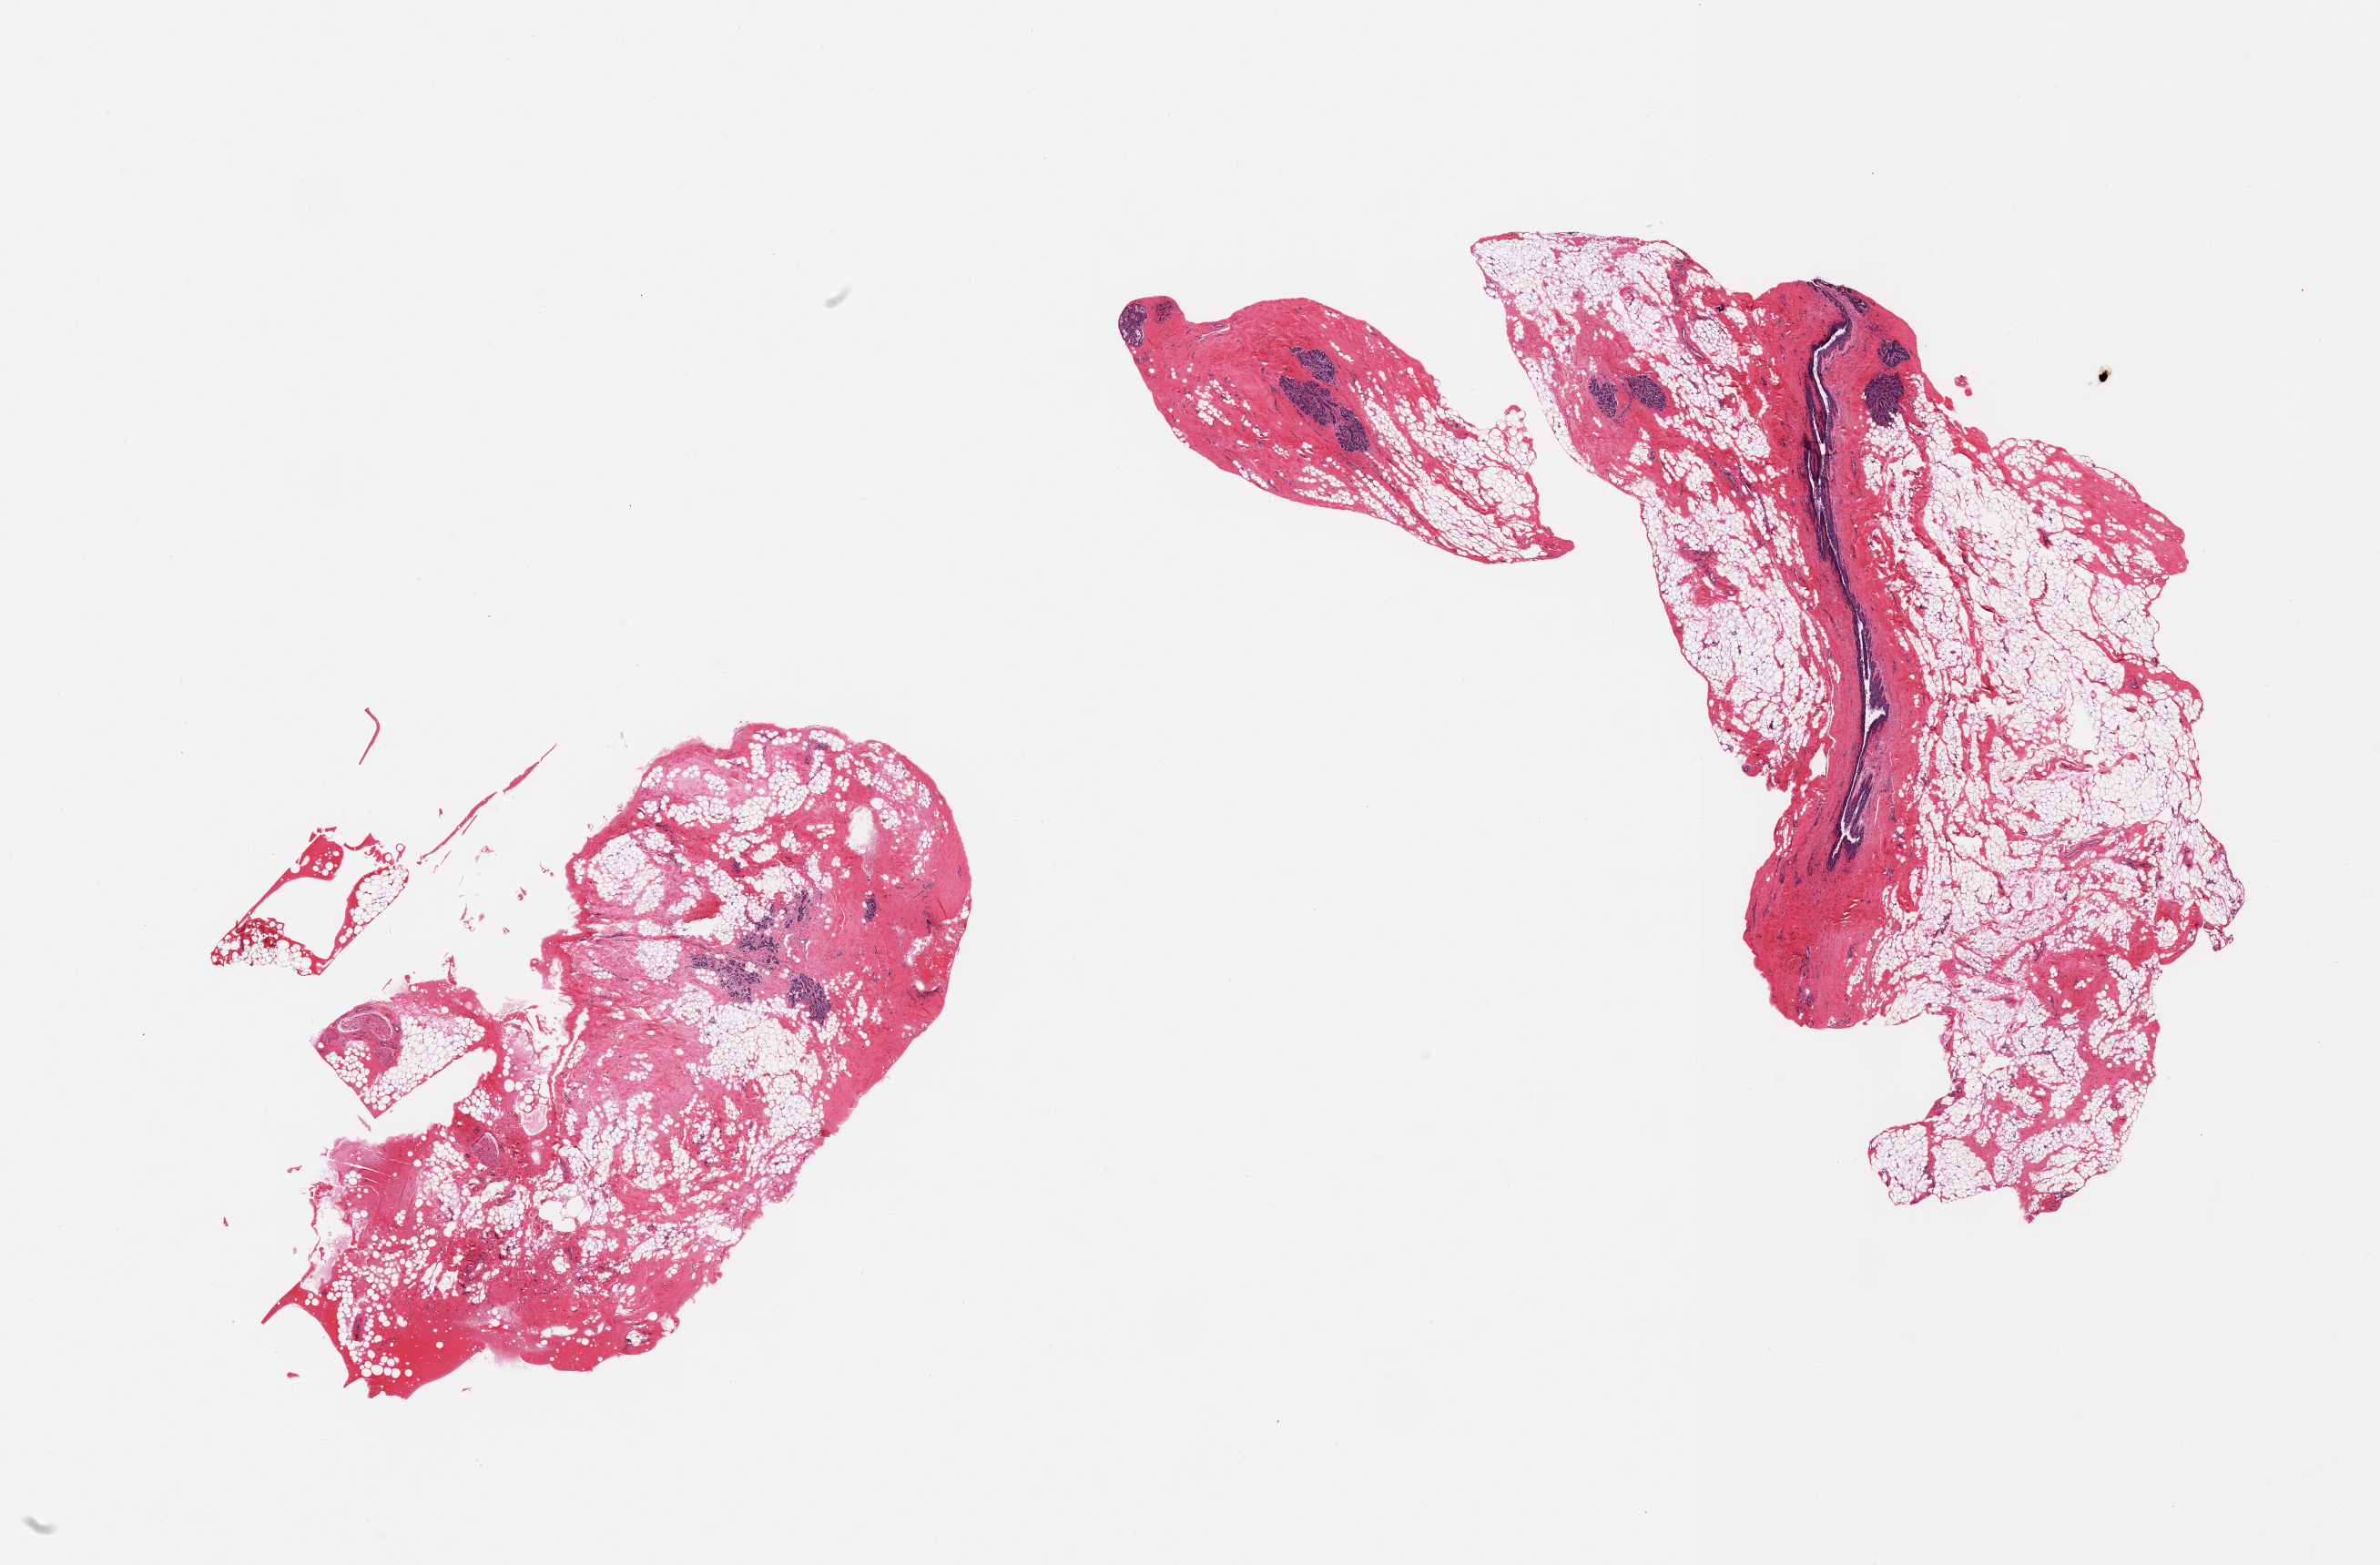
Whole-slide image, hematoxylin and eosin (H&E) stain, low-resolution overview of the scanned area, about 20.7 x 13.6 mm. PAXgene-fixed paraffin-embedded (PFPE) section. Sampled site (target tissue): breast. Tissue donor sample.
Reviewer comment on this tissue sample: 2 pieces; fibroadipose tissue with mammary lobules and duct.